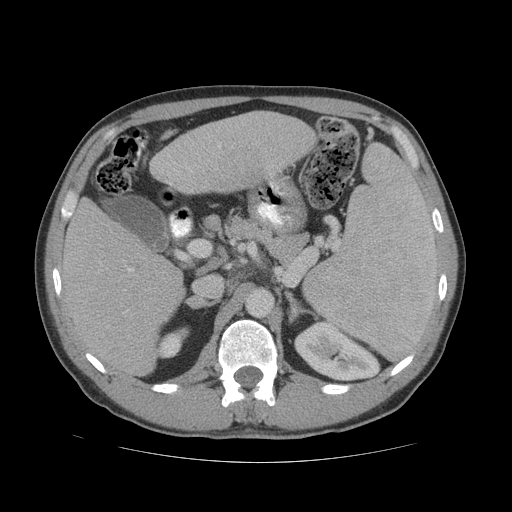
Contrast-enhanced abdominal CT (liver protocol), one axial slice. Reconstruction kernel STANDARD. 140 kVp. Soft-tissue window (W 400 / L 40 HU). 2.5 mm slice thickness. 512 × 512 image matrix. From the clinical record (not read from this slice): diagnosis: hepatocellular carcinoma (patient treated with transarterial chemoembolisation; whether this scan precedes or follows treatment is not stated here); TNM stage (as recorded): Stage-IVB; Child-Pugh class: B; tumour differentiation: well differentiated.
Structures marked on this image (semi-automatic segmentation, software-assisted and operator-edited):
- liver parenchyma outside the tumour (the mass and vessels are separate outlines, so this box may not span the whole liver): bounding box [x1, y1, x2, y2] px = [60, 110, 316, 376]
- liver vessels: [124, 142, 221, 313]